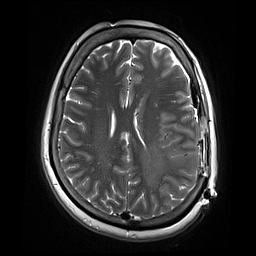
Brain MRI from a brain-tumour surgery series, one axial slice; position 29 of 70 along the scan axis; 2 mm slice thickness; 256 × 256 image matrix, field of view 220 × 220 mm. Case-level facts recorded for this patient, not image findings: histopathology: Glioblastoma; WHO grade: 4.
Annotated regions visible in this slice (expert manual segmentation):
- residual tumour: bounding box [x1, y1, x2, y2] px = [159, 118, 171, 130]